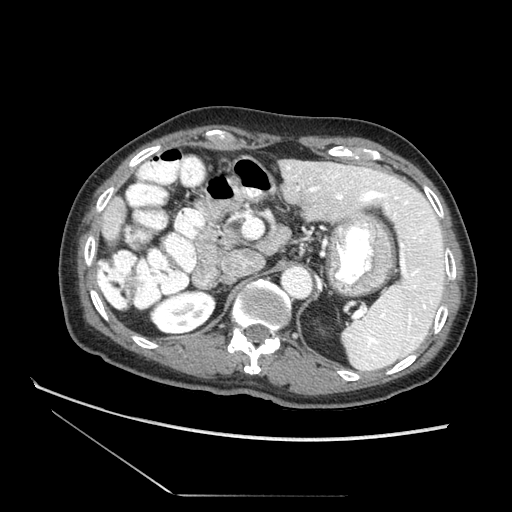
Contrast-enhanced abdominal CT (liver protocol), one axial slice; slice 46 of 73 in the series (ordered by position); reconstruction kernel STANDARD; soft-tissue window (W 400 / L 40 HU); 2.5 mm slice thickness; 512 × 512 image matrix, field of view 360 × 360 mm. From the clinical record (not read from this slice): diagnosis: hepatocellular carcinoma (patient treated with transarterial chemoembolisation; whether this scan precedes or follows treatment is not stated here); TNM stage (as recorded): Stage-II; Child-Pugh class: A; tumour differentiation: moderately differentiated; tumour nodularity: multinodular.
Annotated regions visible in this slice (semi-automatic segmentation, software-assisted and operator-edited):
- liver parenchyma outside the tumour (the mass and vessels are separate outlines, so this box may not span the whole liver): bounding box [x1, y1, x2, y2] px = [108, 160, 448, 354]
- liver vessels: [315, 184, 433, 310]